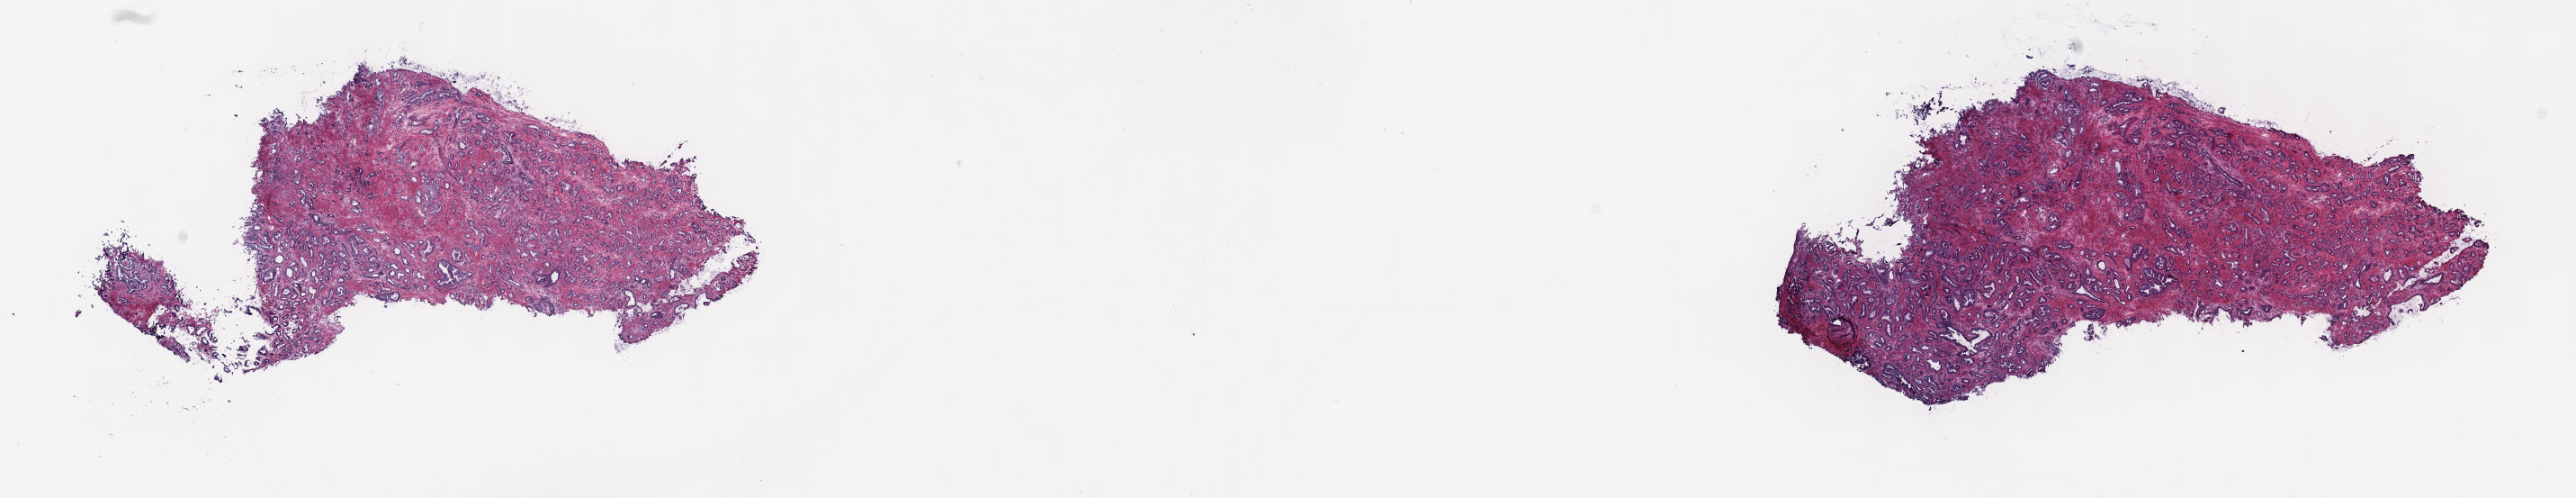
Digitized H&E tissue section (whole slide) — whole scanned area (about 23.2 x 4.5 mm) shown as a low-resolution overview; frozen section from the top of the tissue portion; prostate, primary tumour sample. Male, age 64 years at initial diagnosis. Gleason score: 7 (4+3). Pathologist review of this section (percent, as recorded): tumour cells 60%, tumour nuclei 70%, normal cells 30%, stromal cells 10%, necrosis 0%. Infiltration values recorded for this section: lymphocyte infiltration 0%, monocyte infiltration 0%, neutrophil infiltration 0%.
• laterality: bilateral
• diagnosis: Adenocarcinoma, NOS (prostate gland)
• lymph nodes positive (case pathology): 0 of 4 examined